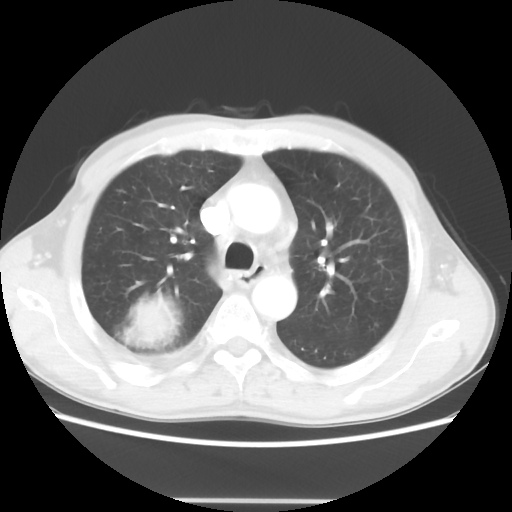
Chest CT, one axial slice; 100 kVp; lung window (W 1500 / L -600 HU); 512 × 512 image matrix, field of view 361 × 361 mm. Patient: male, 66 years. From the clinical record (not read from this slice): clinical TNM (as recorded): T4 N1 M1; histopathological grade: G3.
Annotated regions visible in this slice (bounding box drawn by a radiologist):
- lung tumour (recorded histology: small cell carcinoma): bounding box <129,295,183,348> (left, top, right, bottom; pixels)